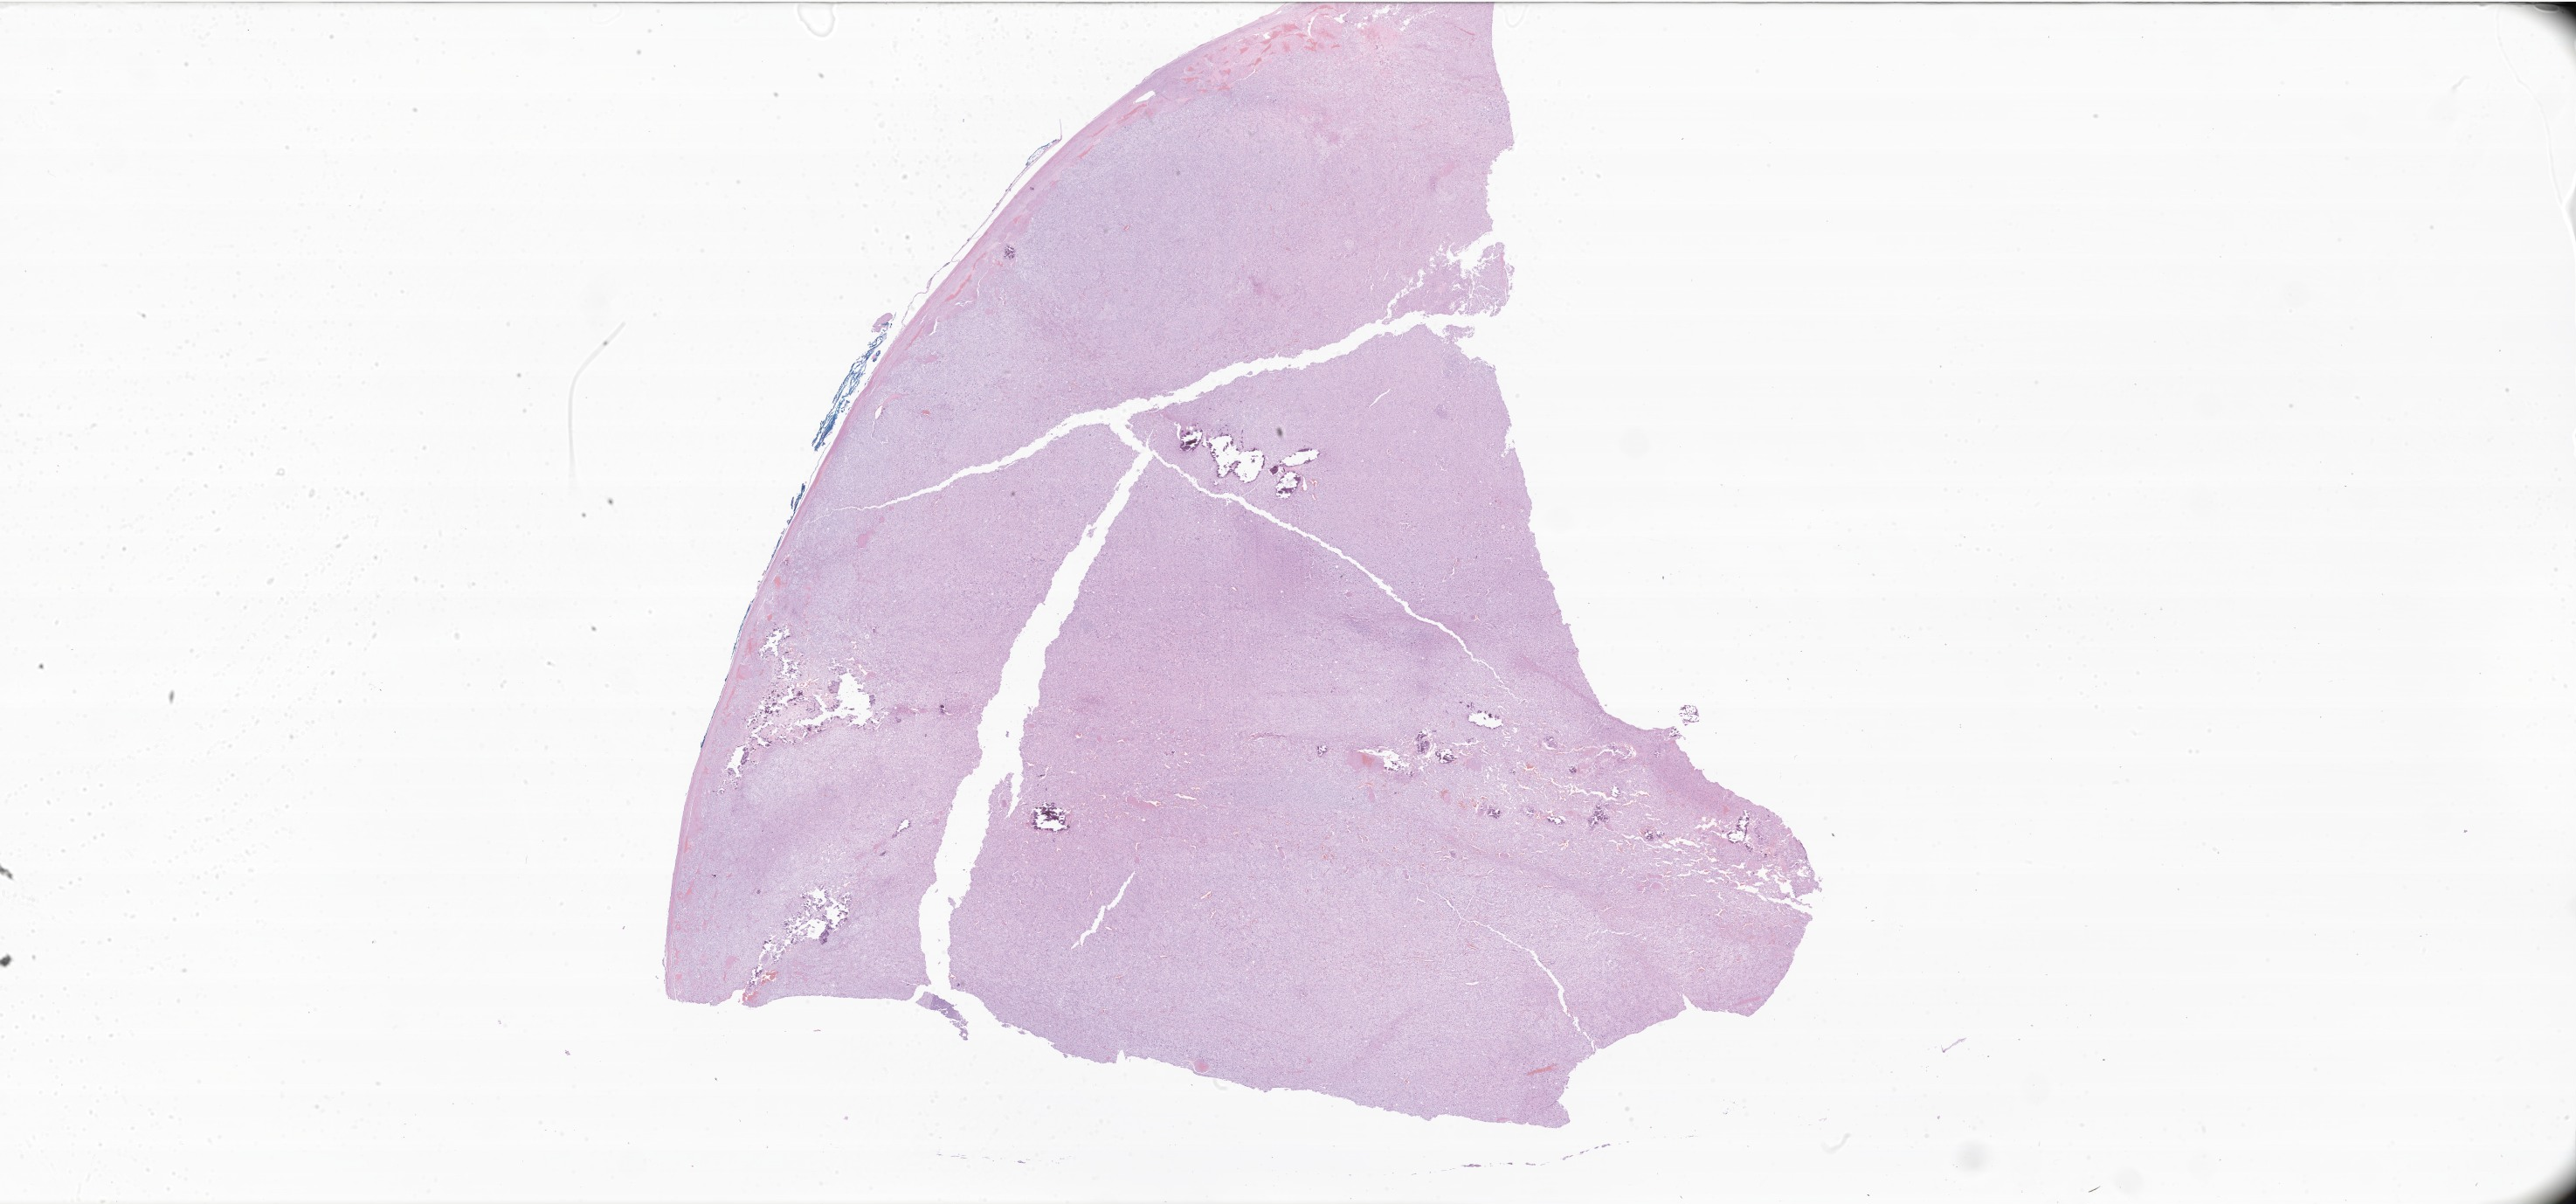
Whole-slide image, haematoxylin and eosin stain of tumor tissue from the adrenal gland, a low-resolution overview of the entire scanned area, about 49.7 x 23.2 mm, formalin-fixed, paraffin-embedded (FFPE) tissue. Patient male; age 74 months (6 years 2 months).
Diagnosis: Carcinoma, NOS.